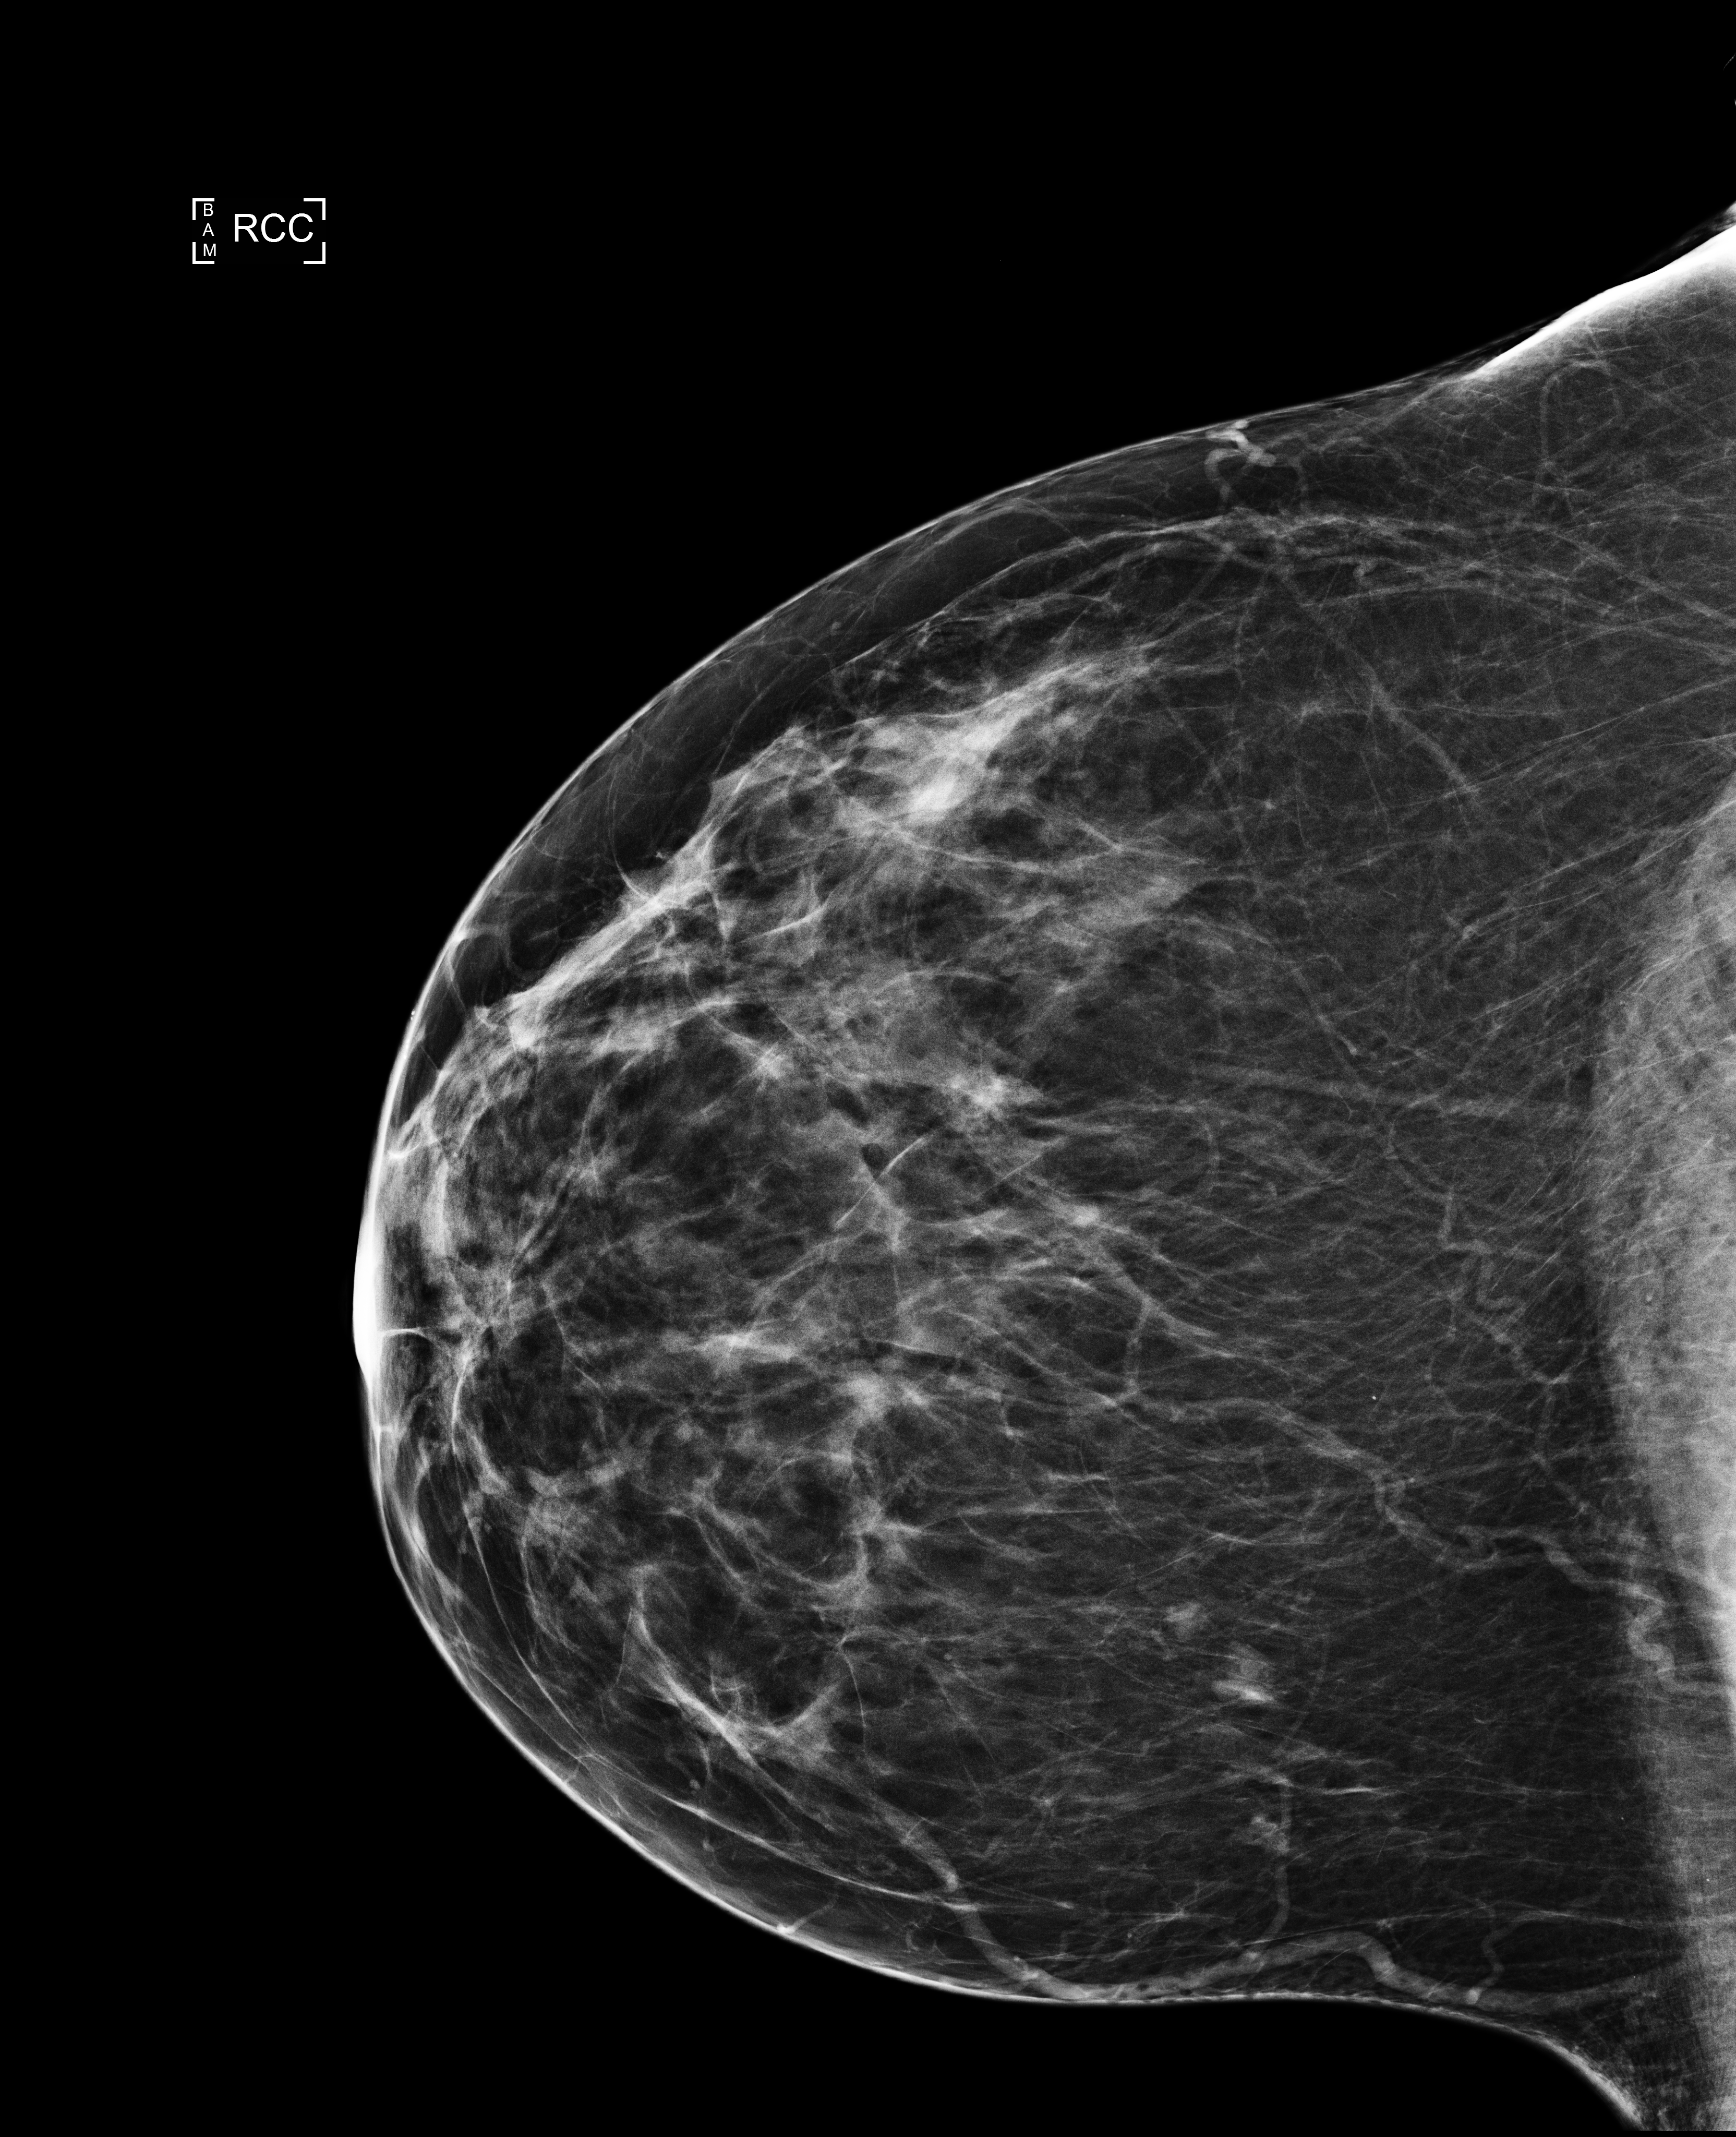
Screening examination. Patient: female, 47 years.
Image type: full-field digital mammogram. Breast: right. Projection: CC view.